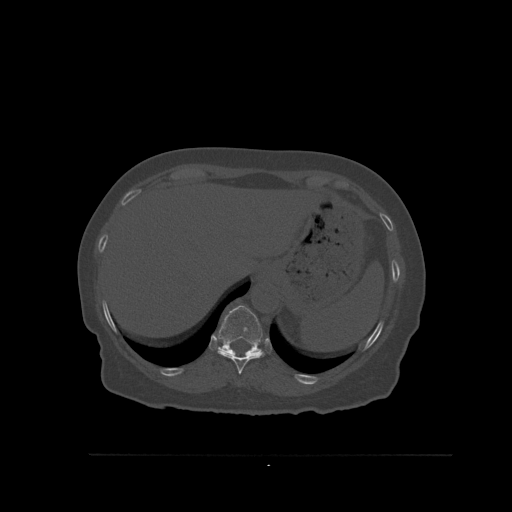
CT including the spine, one axial slice. Slice 313 of 527 in the series (ordered by position). Bone window (W 1800 / L 400 HU). 1.5 mm slice thickness. 512 × 512 image matrix. Female patient, age 73 years. Case-level facts recorded for this patient, not image findings: primary cancer: breast; vertebrae with lytic lesions (as recorded): L2.
Annotated regions visible in this slice (semi-automatic segmentation, software-assisted and operator-edited):
- T10 vertebra: bounding box <217,347,265,374> (left, top, right, bottom; pixels)
- T11 vertebra: <219,305,264,357>